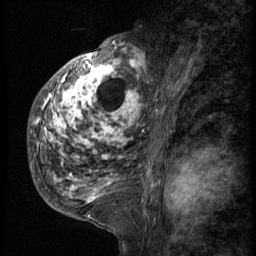
Breast MRI (dynamic contrast-enhanced), one sagittal slice; position 33 of 58 along the scan axis; 3 images stored at this slice position (order not interpretable as contrast timing); 1.5 T; TE 4.2 ms, TR 9 ms; 2.5 mm slice thickness; 256 × 256 image matrix, field of view 180 × 180 mm. Patient: female, 50 years. Case-level facts recorded for this patient, not image findings: setting: breast cancer imaged before/during neoadjuvant chemotherapy; receptor status: triple-negative.
Annotated regions visible in this slice (semi-automatic segmentation, software-assisted and operator-edited):
- analysis volume of interest (the breast-tissue region the enhancement analysis was run in; not a lesion): bounding box (x1, y1, x2, y2) in pixels: (28, 48, 145, 214)
- tumour enhancement mask (voxels above the 140 % enhancement threshold inside the analysis volume of interest): (32, 48, 145, 202)